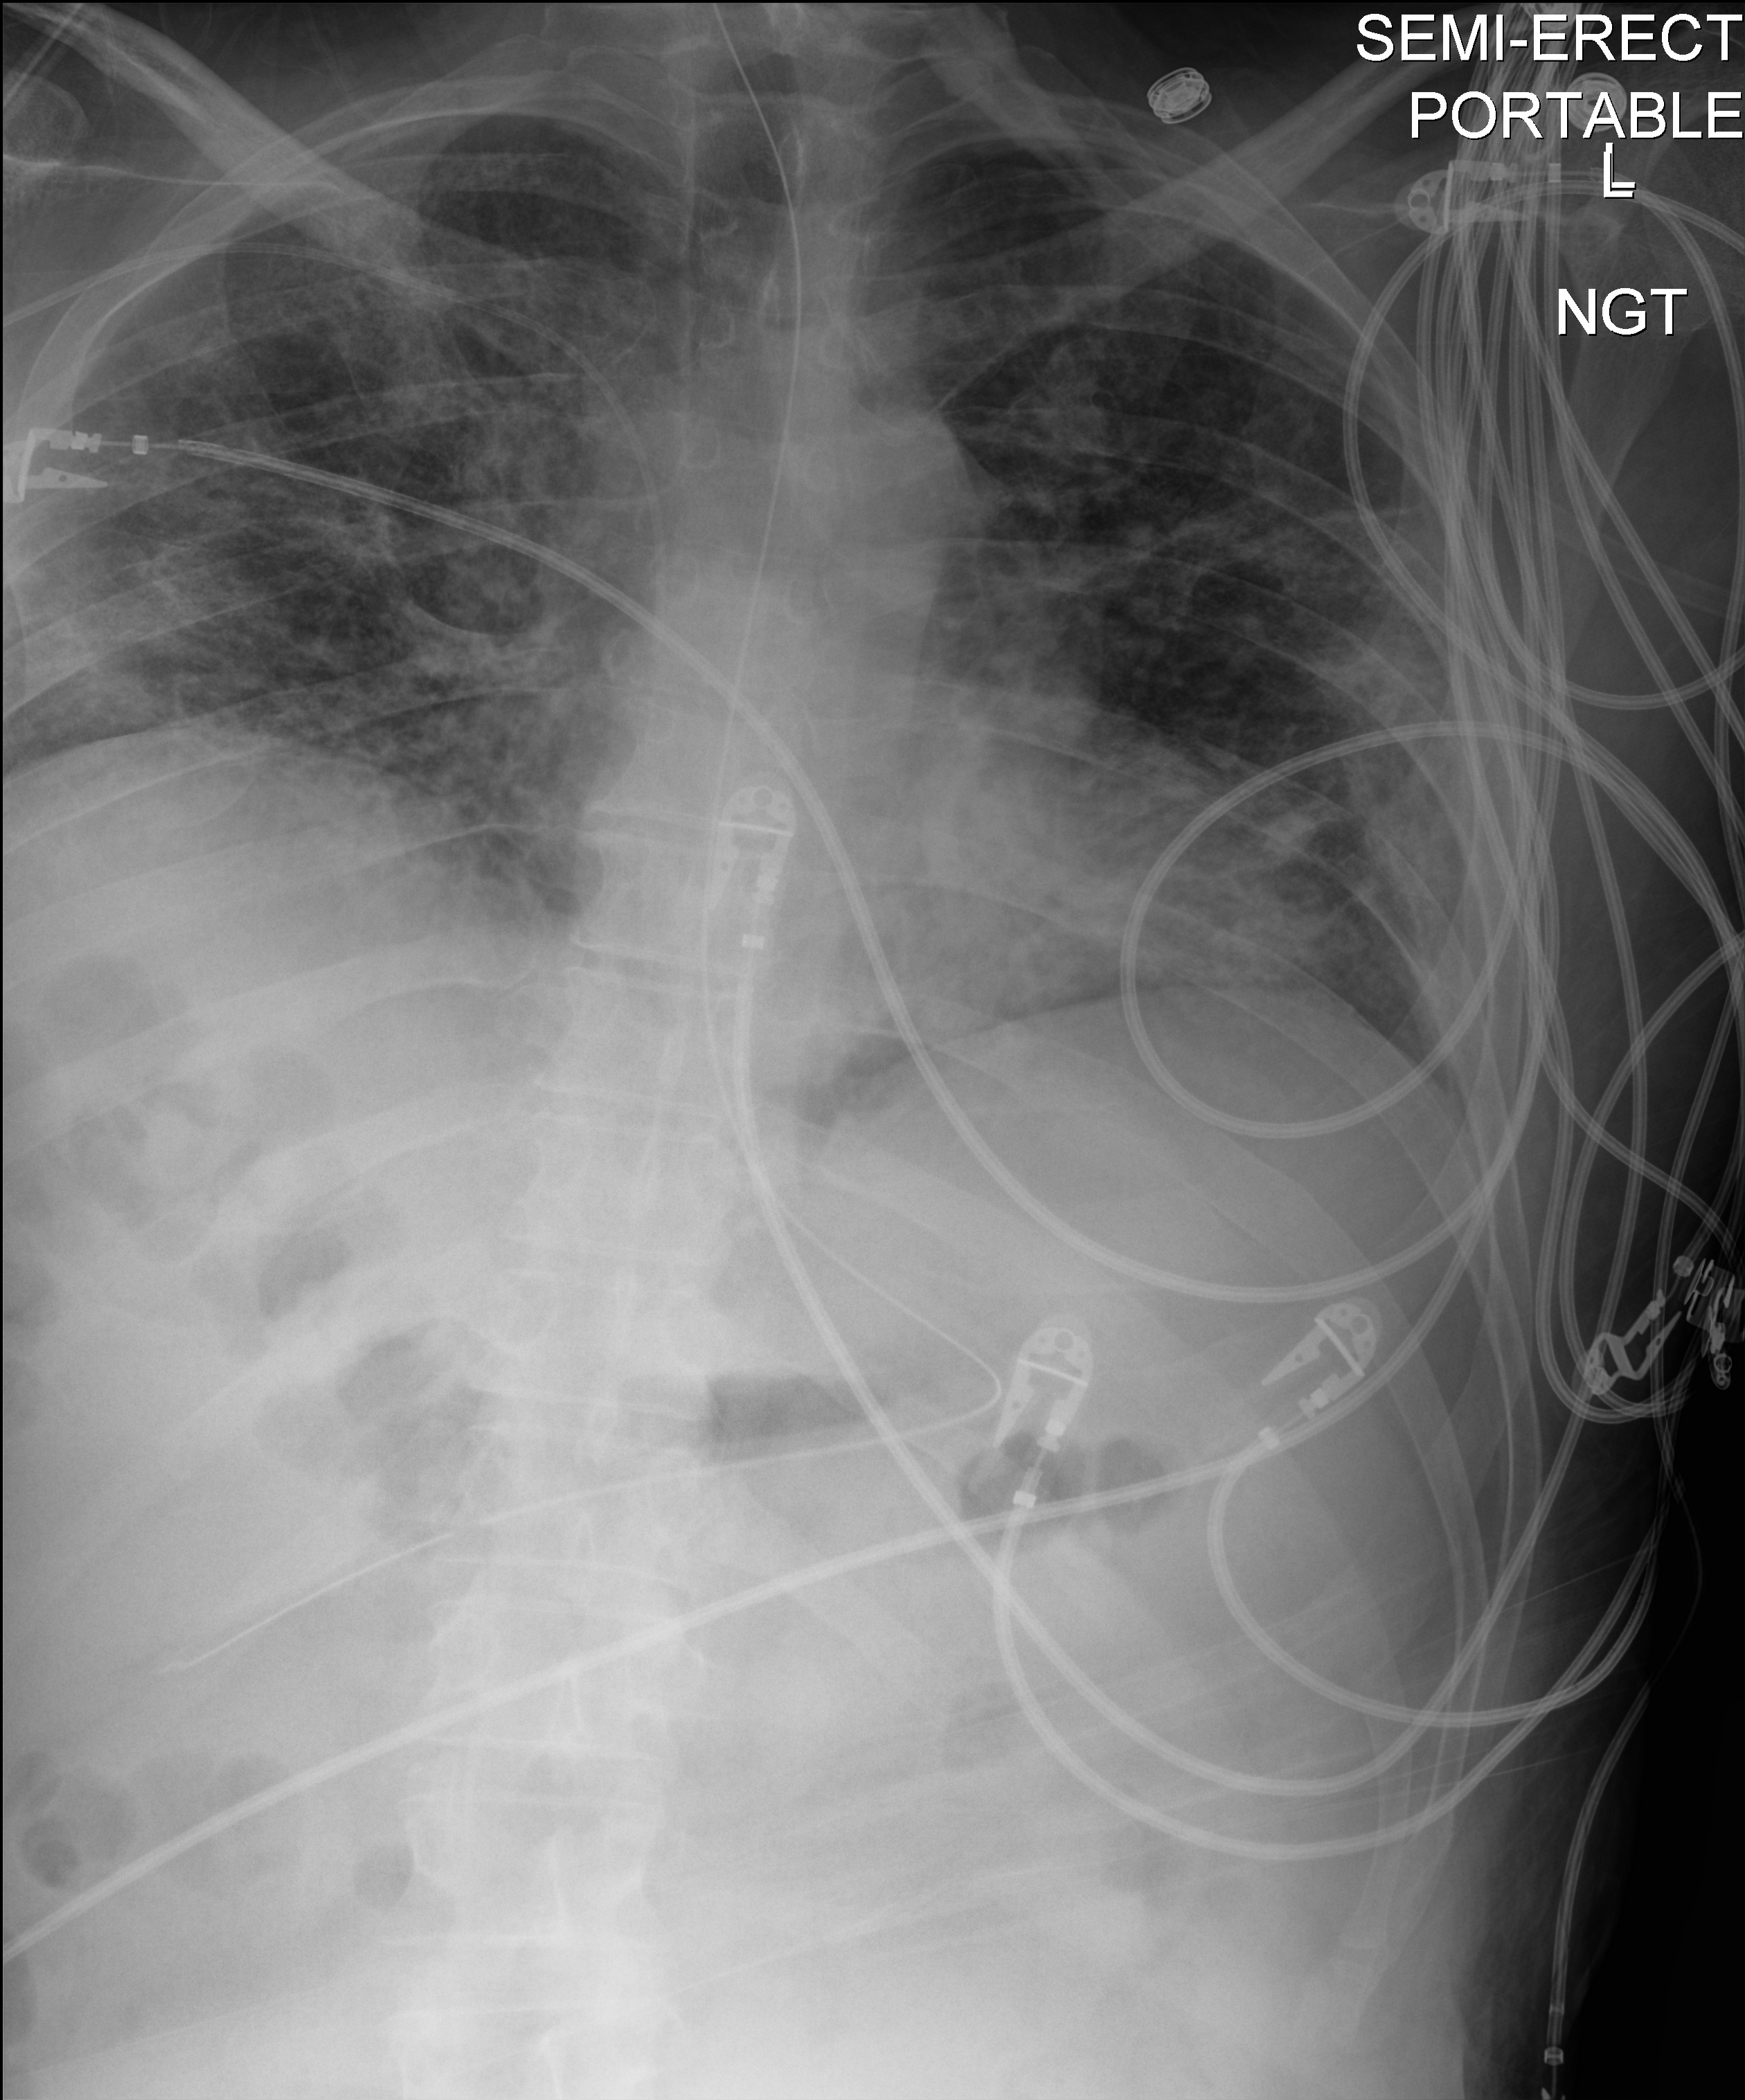
Portable chest radiograph, anteroposterior (AP) projection. Male patient hospitalised with COVID-19, age 18–59 years.
Hospital-stay facts (about this admission, not read from this image; timing relative to this image not recorded):
- length of hospital stay: 48 days
- mechanically ventilated during this hospital stay: yes
- chronic kidney disease (admission record): no